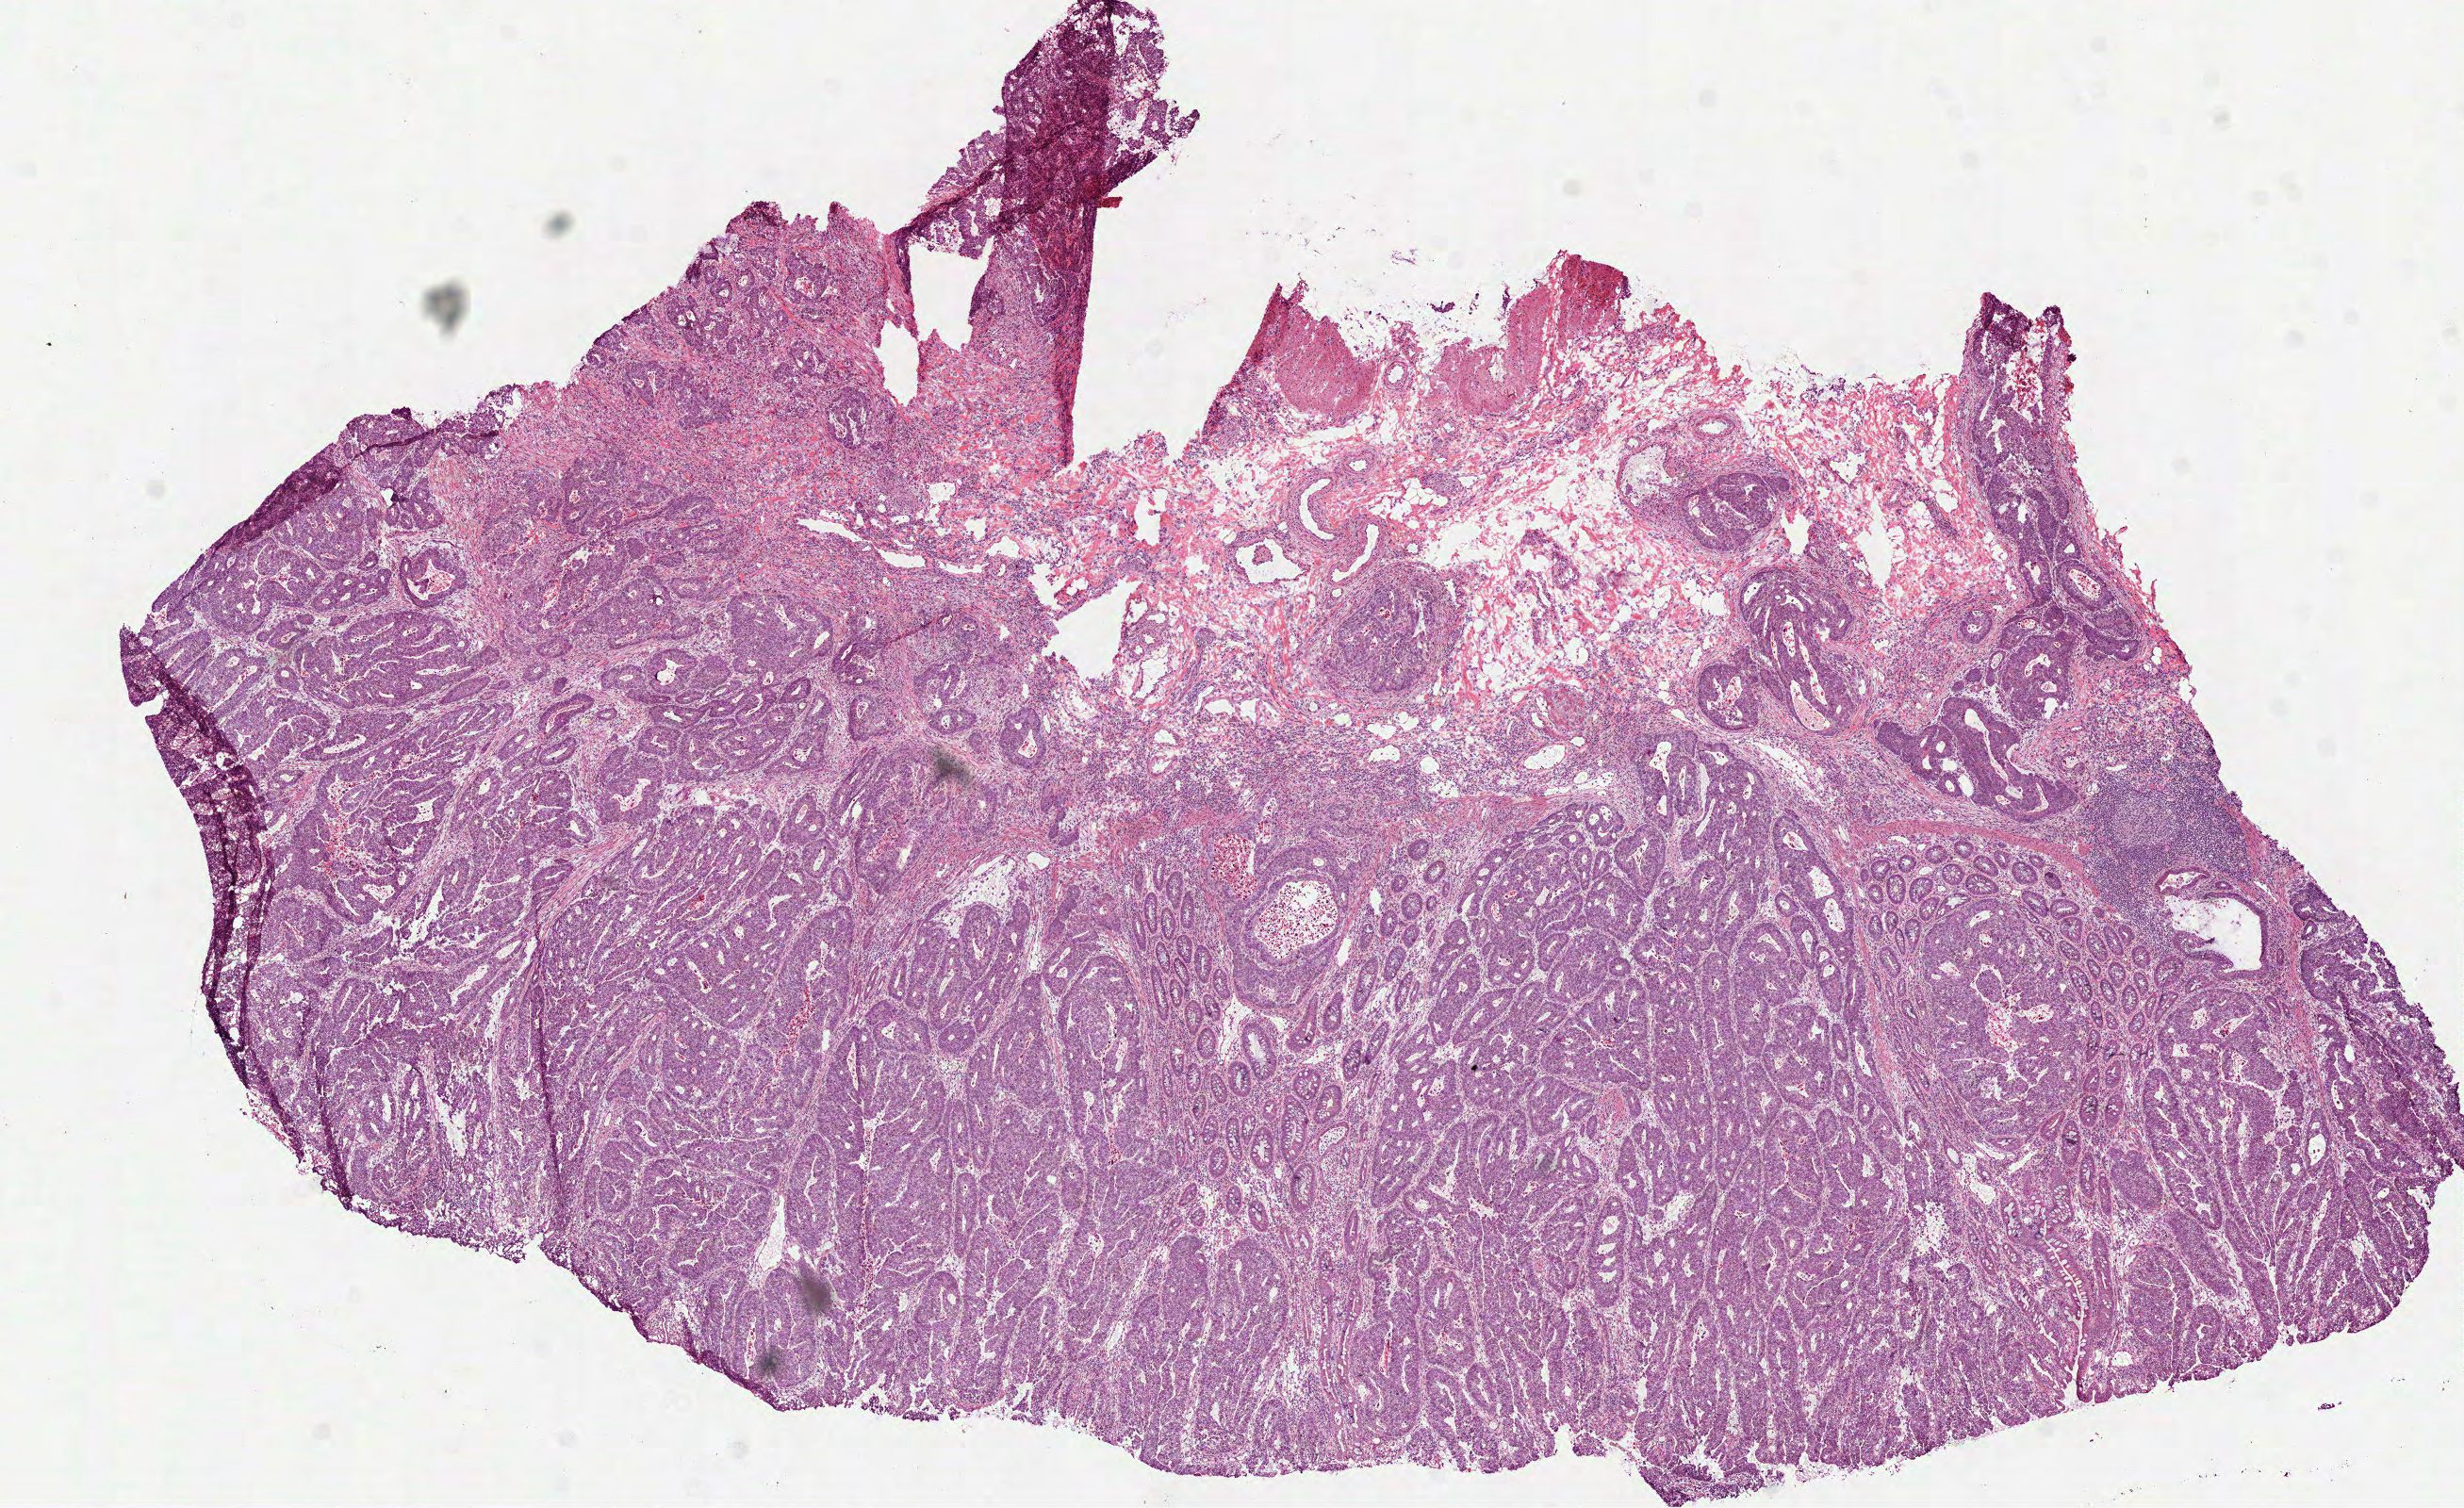
Whole-slide histology image, Hematoxylin and eosin (H&E) stained — low-resolution overview of the scanned area, about 10.5 x 6.5 mm (acquisition: 40x scan); frozen section from the top of the tissue portion; primary tumour sample from the colon. Patient: male, age at initial diagnosis 56 years. Pathologist review of this section (percent, as recorded): tumour cells 90%, tumour nuclei 80%, normal cells 0%, stromal cells 5%, necrosis 5%. Inflammatory infiltration, as recorded: lymphocyte infiltration 7%, monocyte infiltration 2%, neutrophil infiltration 7%.
AJCC pathologic stage: IVA (7th edition). Histologic diagnosis: Adenocarcinoma, NOS (descending colon).